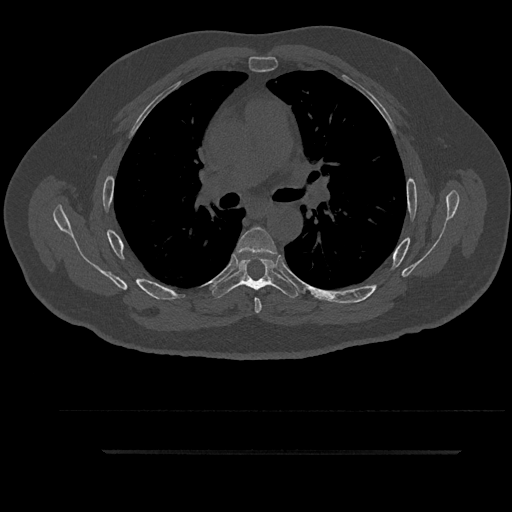
CT including the spine, one axial slice. Slice 599 of 797 in the series (ordered by position). Bone window (W 1800 / L 400 HU). 0.5 mm slice thickness. 512 × 512 image matrix. Patient: male, 63 years. Case-level facts recorded for this patient, not image findings: primary cancer: renal.
Outlined on this slice (semi-automatically segmented with operator editing):
- T5 vertebra: bounding box (x1, y1, x2, y2) in pixels: (235, 227, 278, 313)
- T6 vertebra: (211, 256, 300, 298)